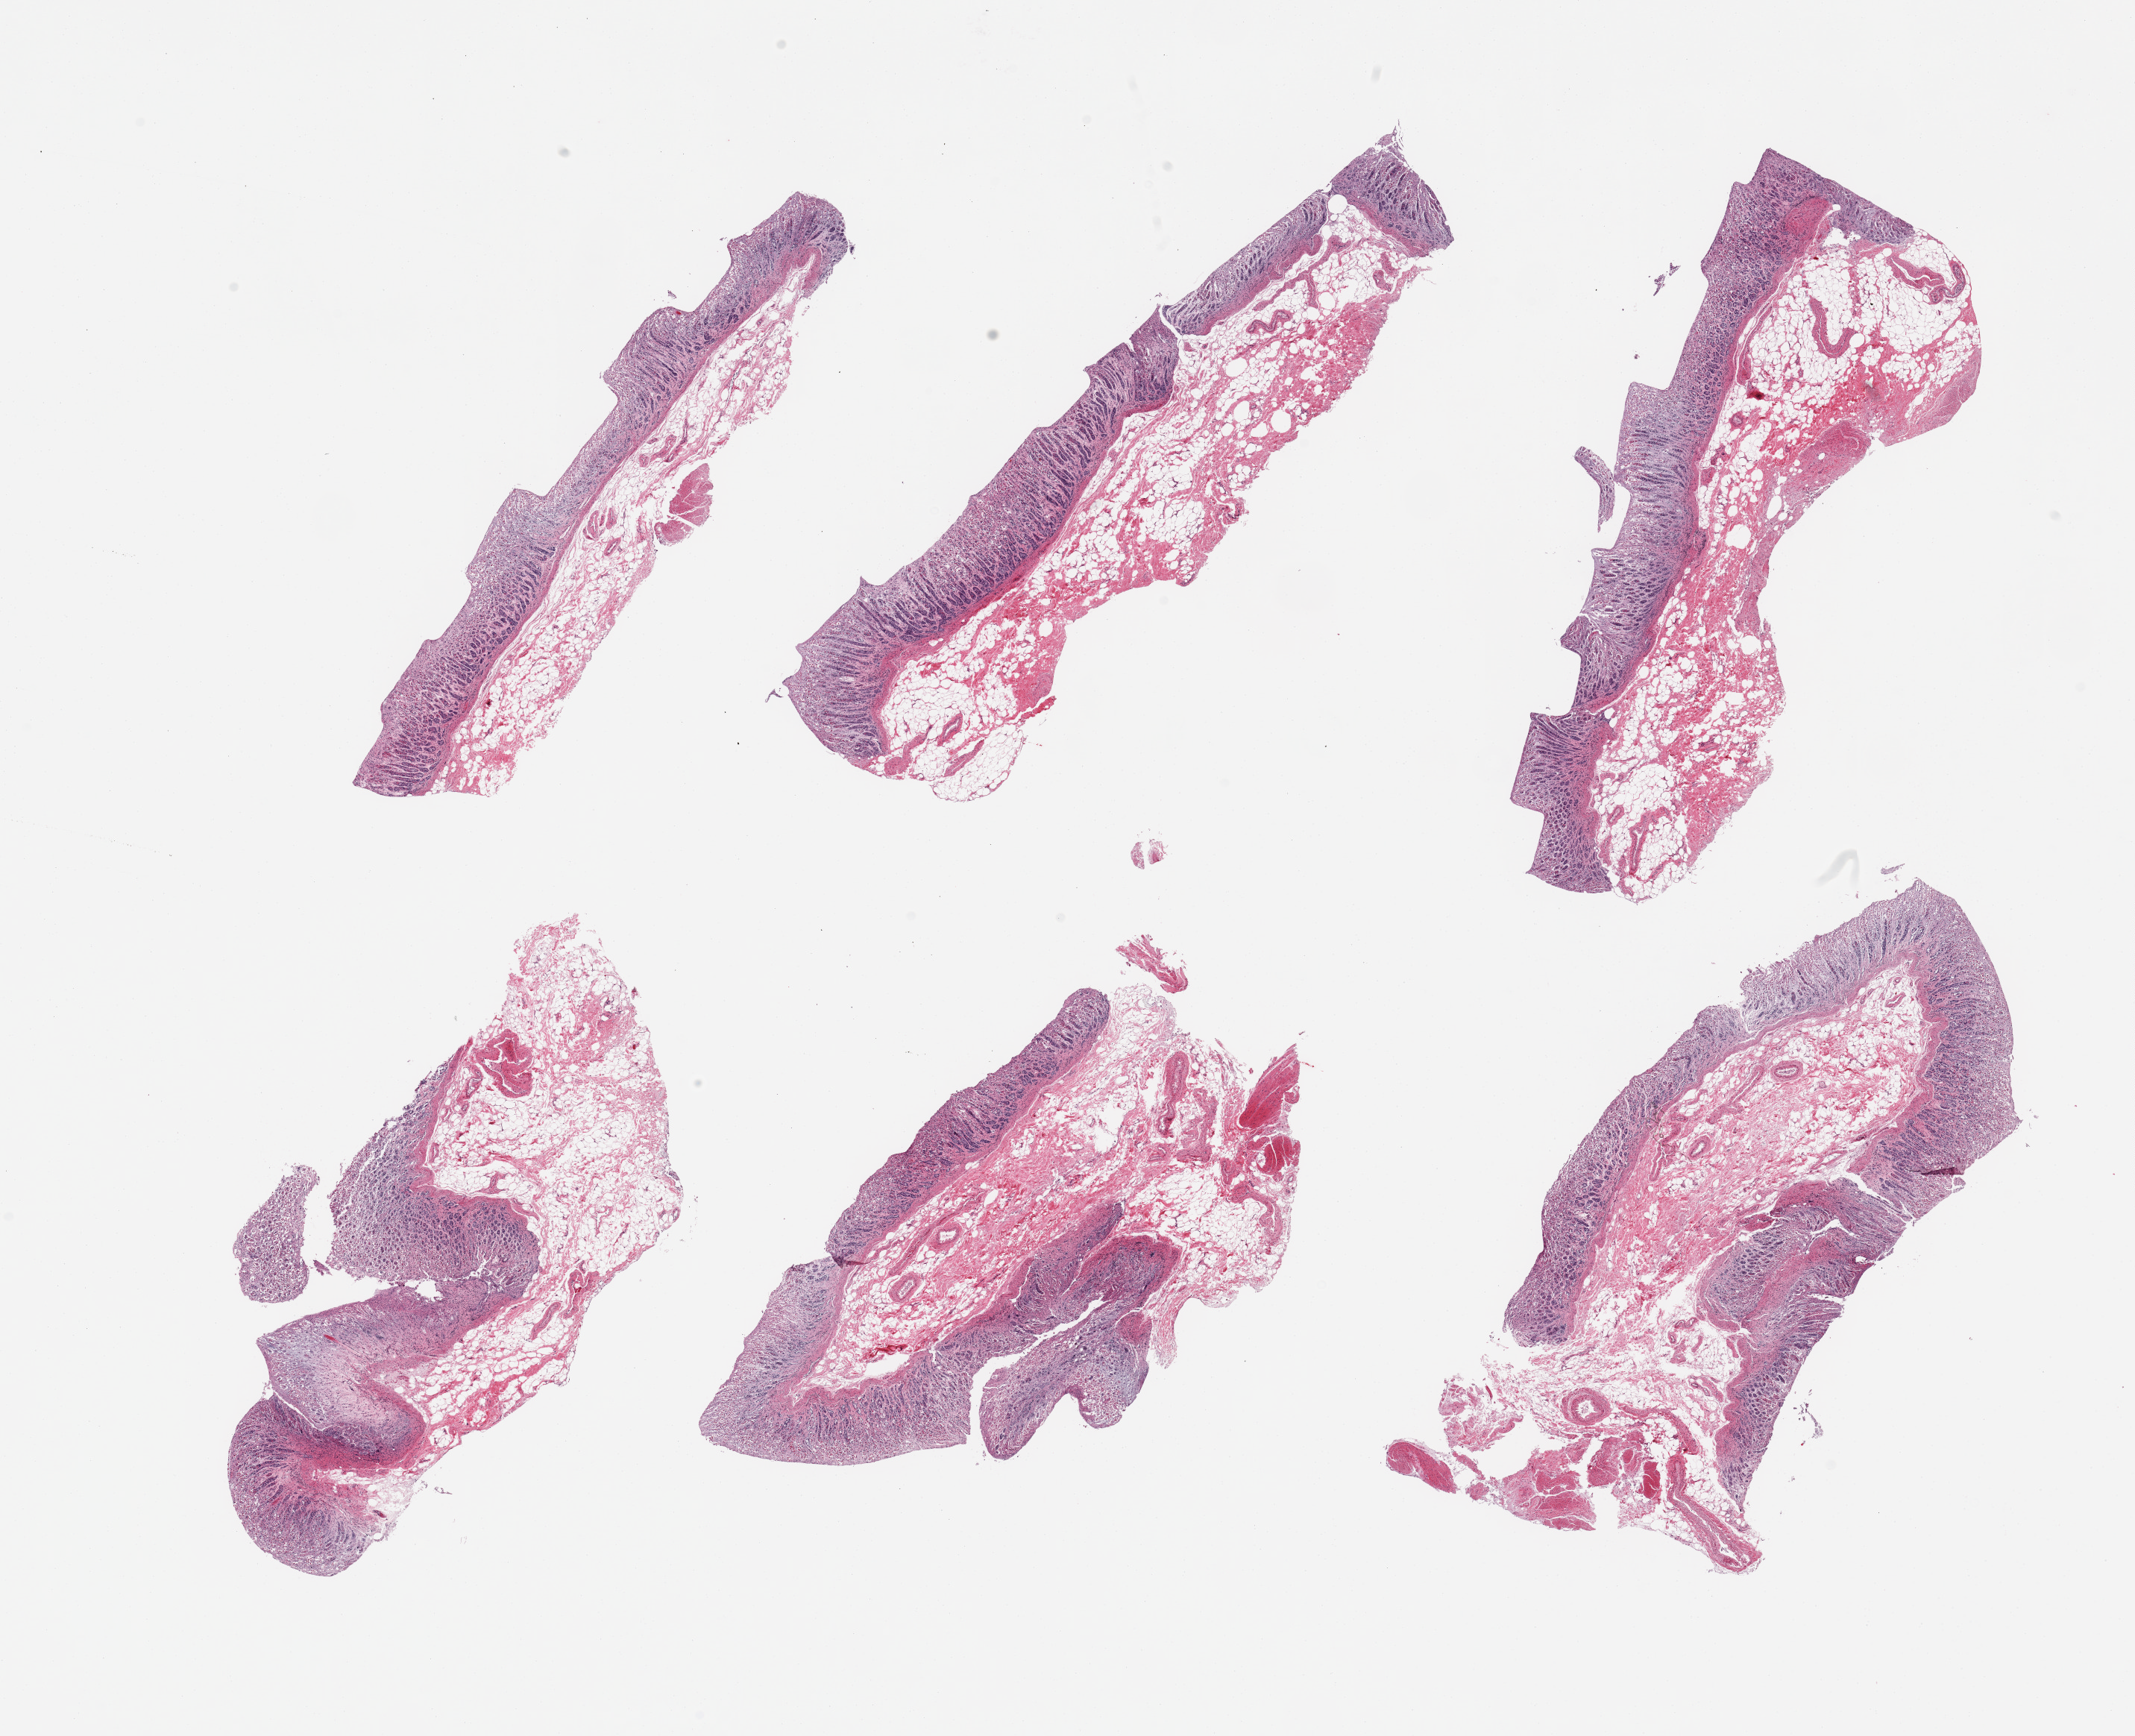
Digitized haematoxylin and eosin-stained section, a low-resolution overview of the entire scanned area, about 22.6 x 18.4 mm; PAXgene-fixed paraffin-embedded (PFPE) section; sampled site (target tissue): stomach; donor tissue sample.
Reviewer comment on this tissue sample: 6 pieces, moderatley autolyzed mucosa with only trivial muscularis (full thickness sections preferred).